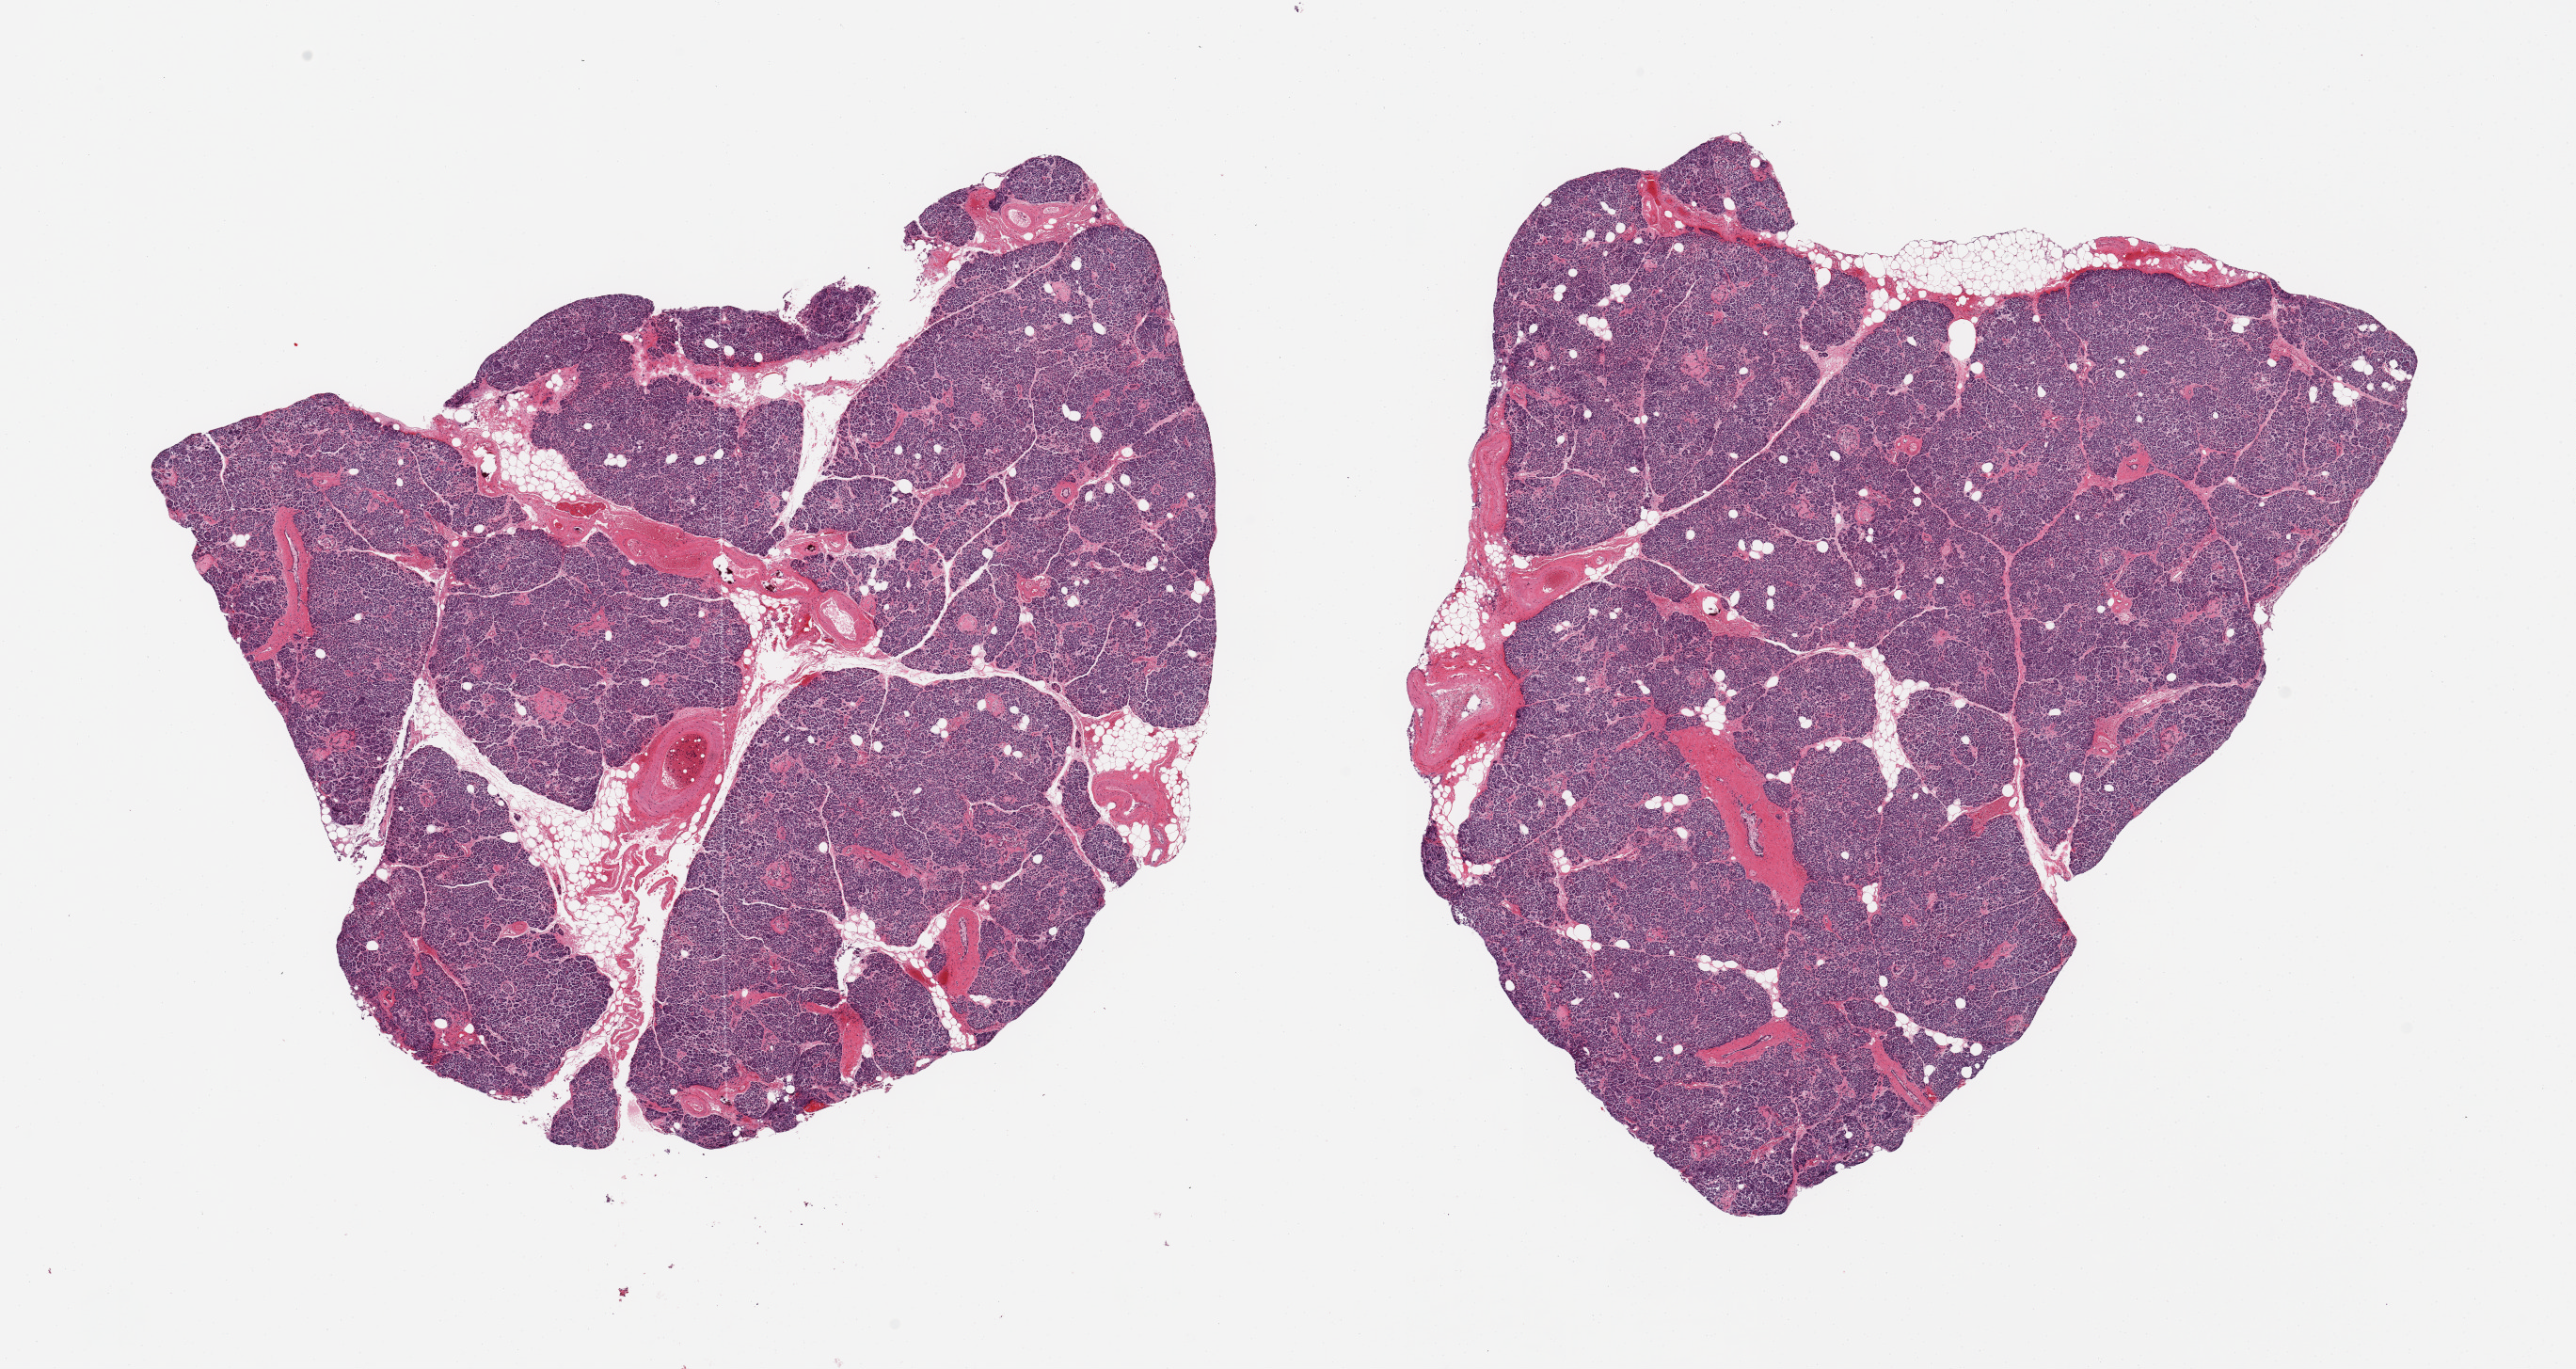
Hematoxylin and eosin (H&E) whole-slide image — whole scanned area (about 21.7 x 11.5 mm) shown as a low-resolution overview; PAXgene-fixed paraffin-embedded (PFPE) section; target tissue: pancreas; donor tissue sample. Donor: female.
• review note (as recorded): 2 pieces; accentuated thick-walled vessels, some hyalinized islets, focal vascular medial calcifications